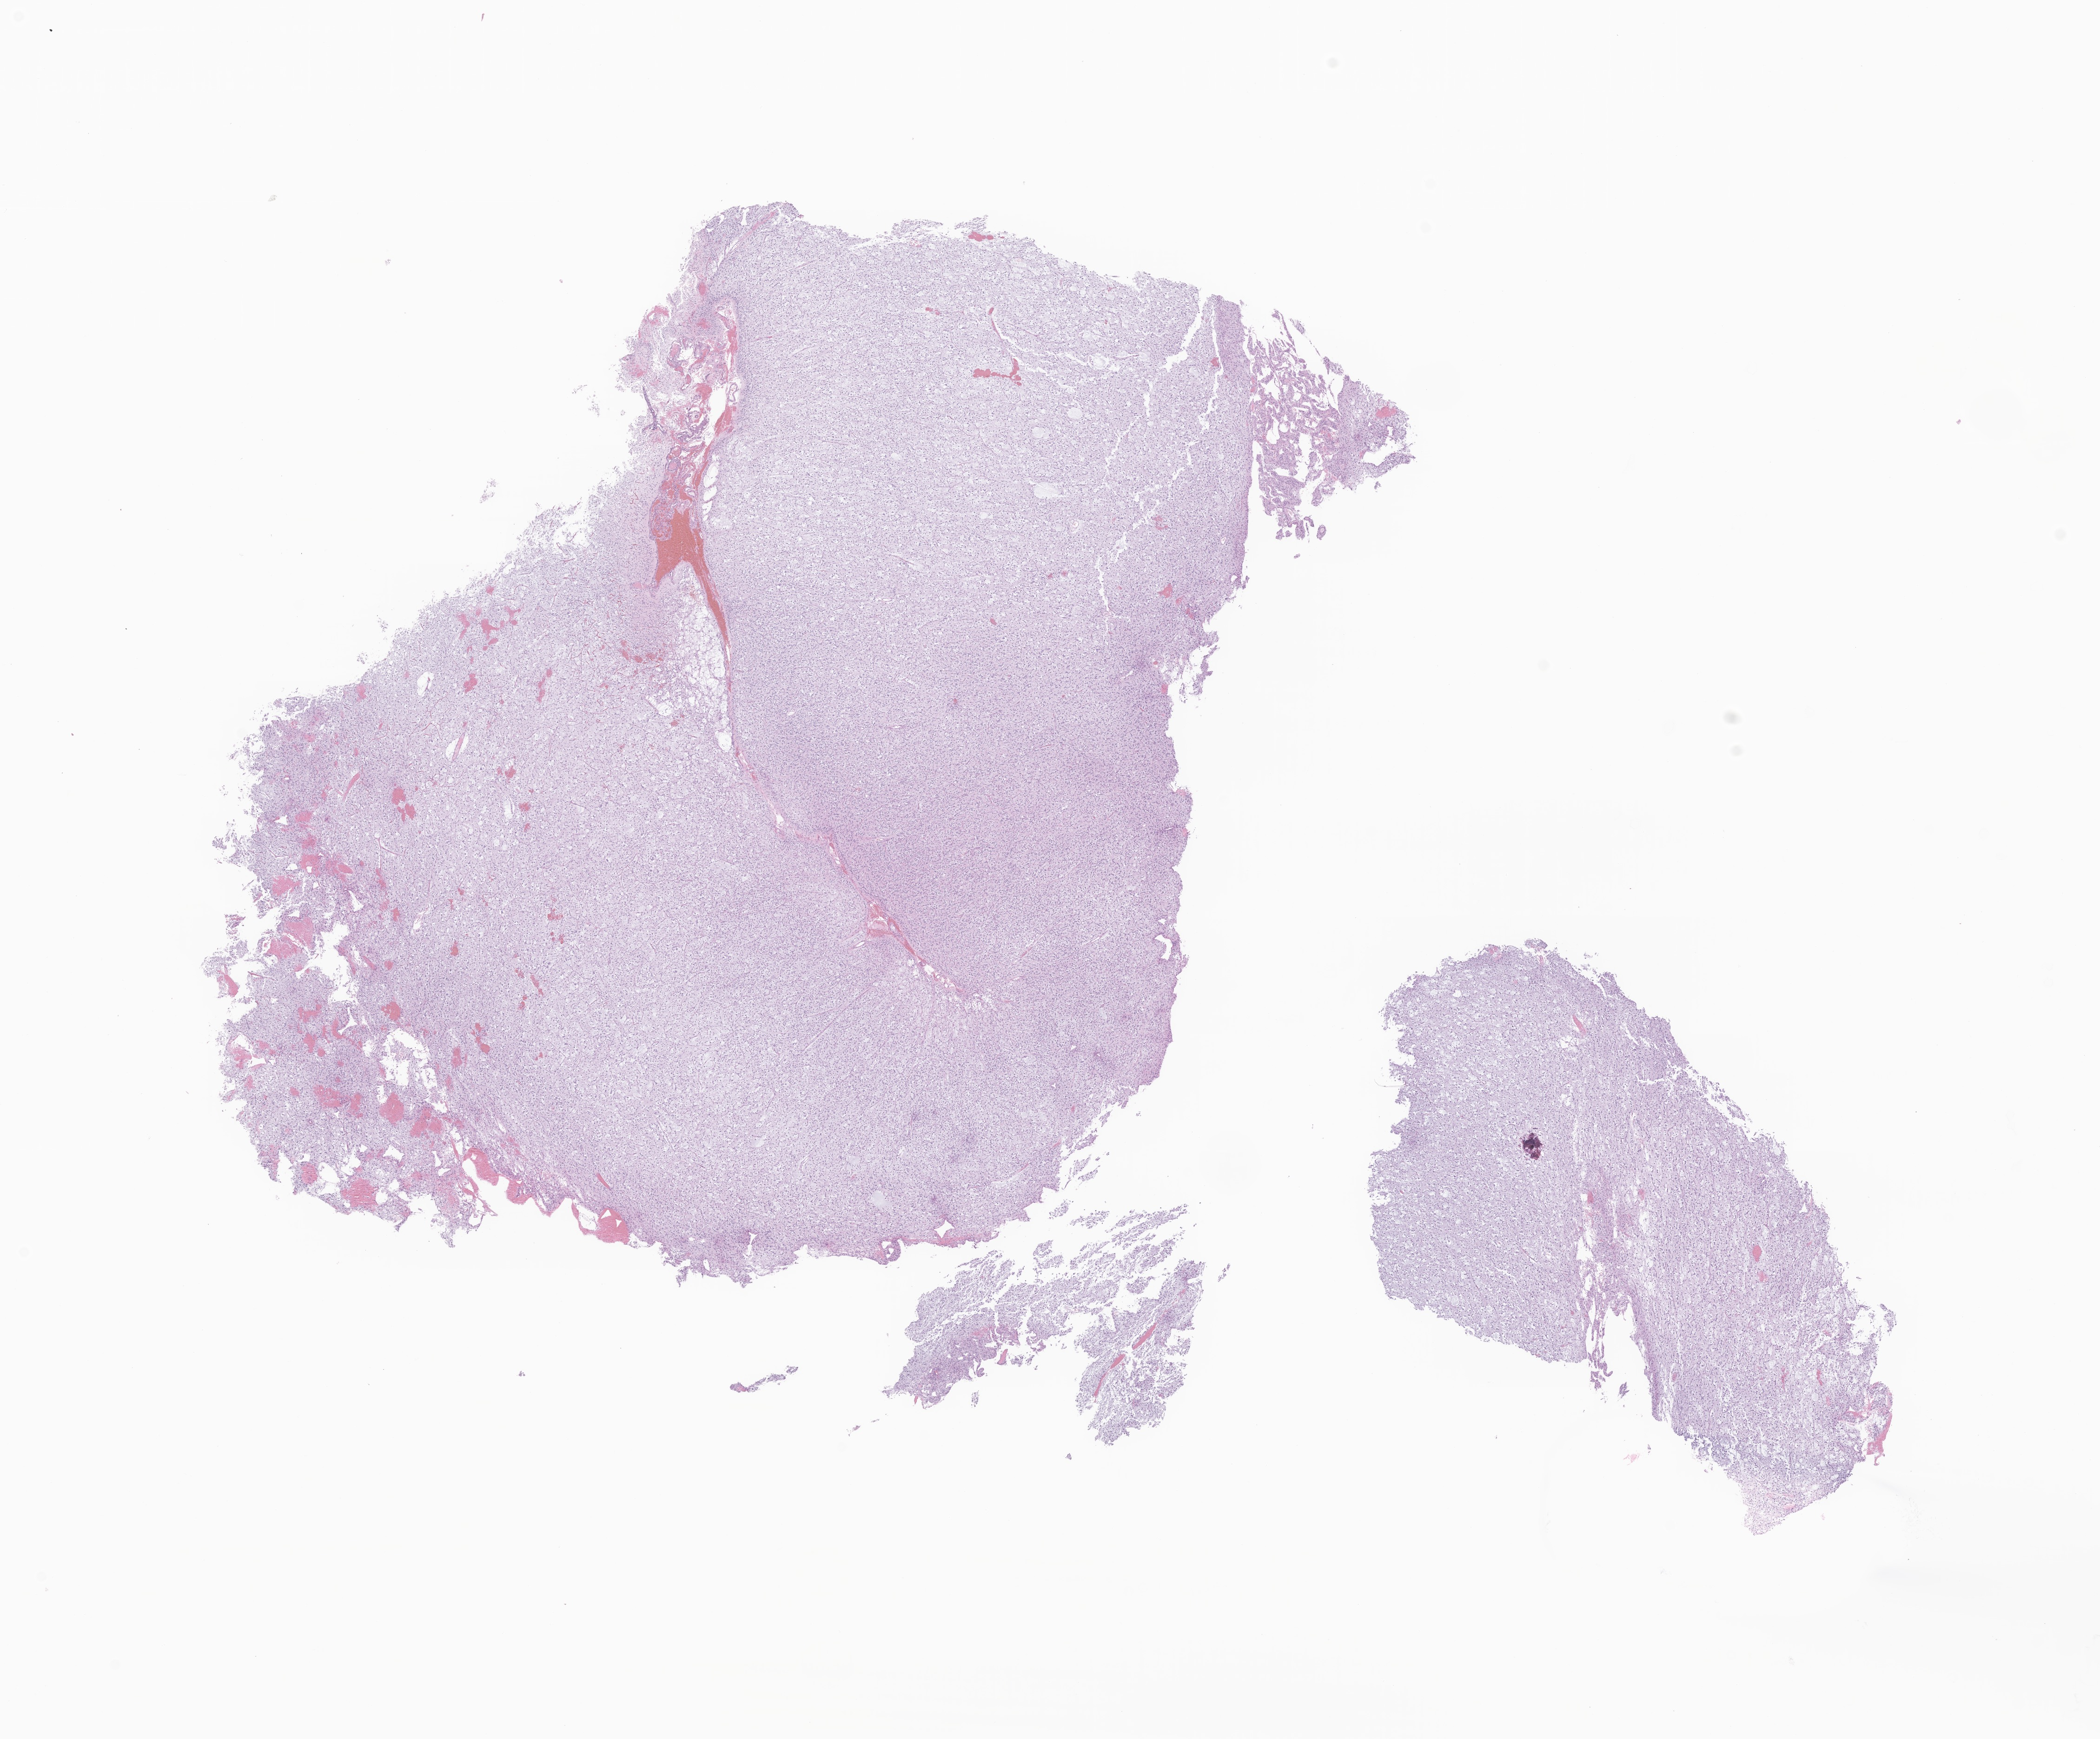
Whole-slide image, H&E stain of tumor tissue from the frontal lobe, shown as a low-resolution overview of the whole scanned area (about 19.0 x 15.8 mm). Formalin-fixed paraffin-embedded section. Patient male; age 963 days (about 2.6 years).
• diagnosis: Dysembryoplastic neuroepithelial tumor